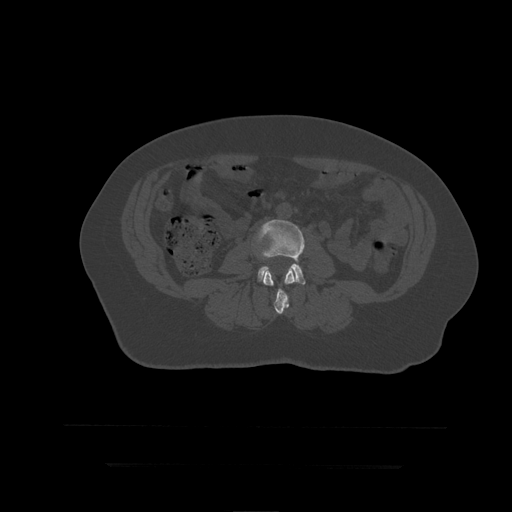
CT including the spine, one axial slice. Position 110 of 399 along the scan axis. Reconstruction kernel STANDARD. 120 kVp. Bone window (W 1800 / L 400 HU). 512 × 512 image matrix, field of view 450 × 450 mm. Patient age 41 years. From the clinical record (not read from this slice): primary cancer: breast.
Structures marked on this image (semi-automatically segmented with operator editing):
- L3 vertebra: bounding box <263,267,296,314> (left, top, right, bottom; pixels)
- L4 vertebra: <258,219,306,285>